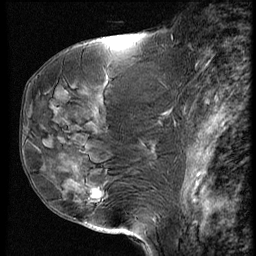
Breast MRI (dynamic contrast-enhanced), one sagittal slice; slice 27 of 60 in the series (ordered by position); dynamic contrast-enhanced series, image 2 of 4 at this slice position (ordered by acquisition); 1.5 T; TE 4.2 ms, TR 9 ms; 256 × 256 image matrix, field of view 180 × 180 mm. Female patient, age 50 years. From the clinical record (not read from this slice): setting: breast cancer imaged before/during neoadjuvant chemotherapy; receptor status: HR-positive, HER2-negative.
Annotated regions visible in this slice (semi-automatic segmentation, software-assisted and operator-edited):
- analysis volume of interest (the breast-tissue region the enhancement analysis was run in; not a lesion): bounding box (x1, y1, x2, y2) in pixels: (48, 109, 135, 230)
- tumour enhancement mask (voxels above the 140 % enhancement threshold inside the analysis volume of interest): (90, 189, 104, 199)